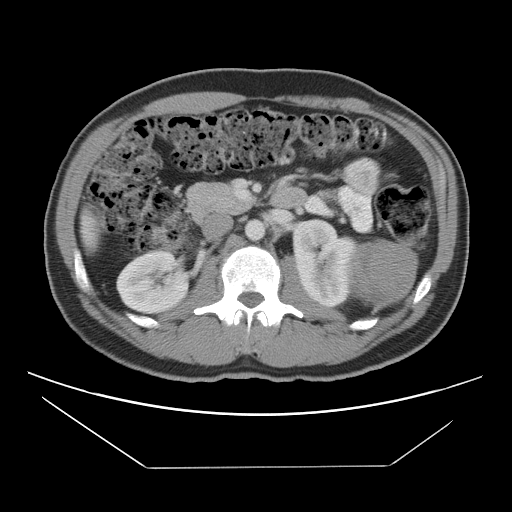
Contrast-enhanced abdominal CT, one axial slice. Slice 62 of 131 in the series (ordered by position). Reconstruction kernel STANDARD. 120 kVp. Intravenous contrast given. Soft-tissue window (W 400 / L 40 HU). 512 × 512 image matrix, field of view 396 × 396 mm. Male patient, age 44 years. Case-level facts recorded for this patient, not image findings: diagnosis: adrenocortical carcinoma; tumour side: left adrenal; tumour size at pathology: 15.5 cm; Ki-67 index: 6 %; stage (as recorded): 2.
Structures marked on this image (semi-automatic segmentation, software-assisted and operator-edited):
- mass: bounding box <350,241,416,303> (left, top, right, bottom; pixels)